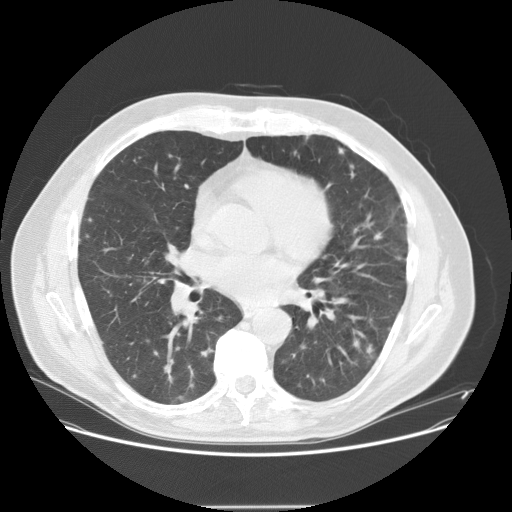
Low-dose screening chest CT, one axial slice. Position 72 of 143 along the scan axis. Lung window (W 1500 / L -600 HU). 2.5 mm slice thickness. 512 × 512 image matrix, field of view 400 × 400 mm.
Structures marked on this image (manually delineated by an expert):
- lesion 7 (tumor): box from (x=366, y=344) to (x=374, y=358) px